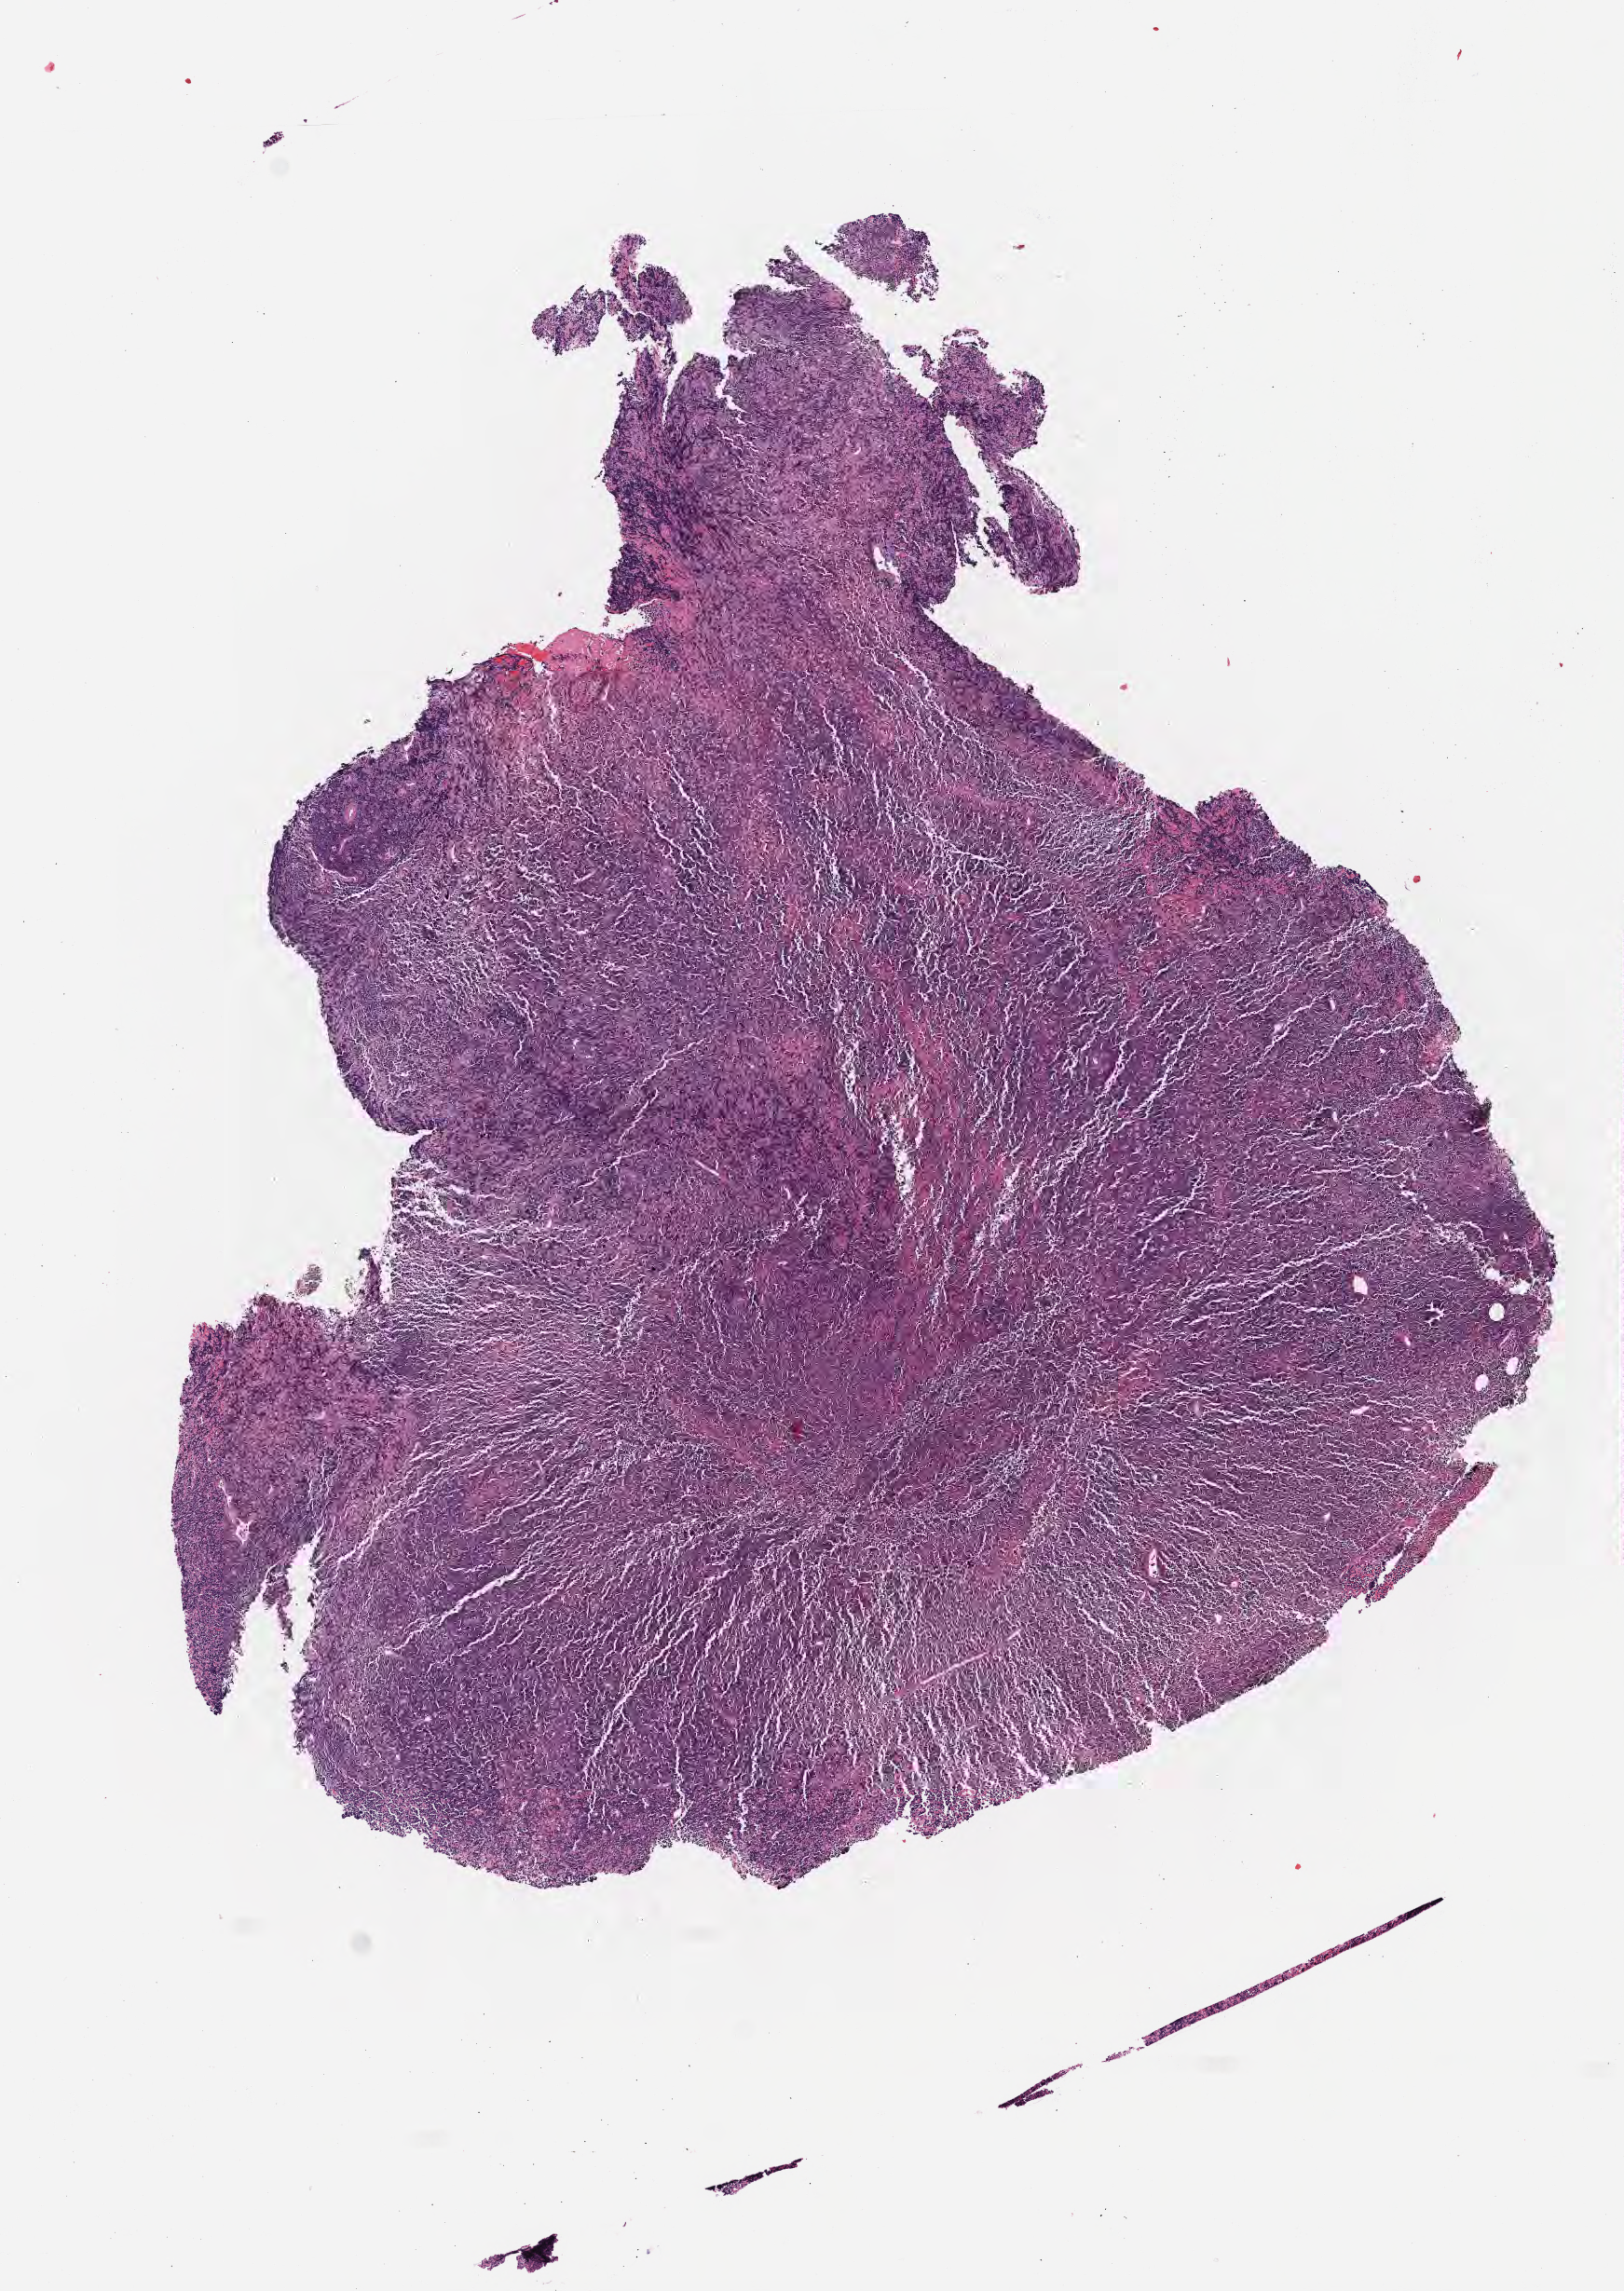
Hematoxylin and eosin (H&E) whole-slide image, a low-resolution overview of the entire scanned area, about 7.0 x 9.9 mm; FFPE section; specimen: primary tumor; site: mandible. Female patient; age at initial diagnosis 5 years. Slide review estimates, as recorded: tumor cells 85%, tumor nuclei 90%, stromal cells 10%, necrosis 5%, normal cells 0%. Inflammatory infiltration, as recorded: lymphocyte infiltration 40%, monocyte infiltration 25%, neutrophil infiltration 5%.
Ann Arbor stage (patient): Stage III. Diagnosis: Burkitt lymphoma, NOS.